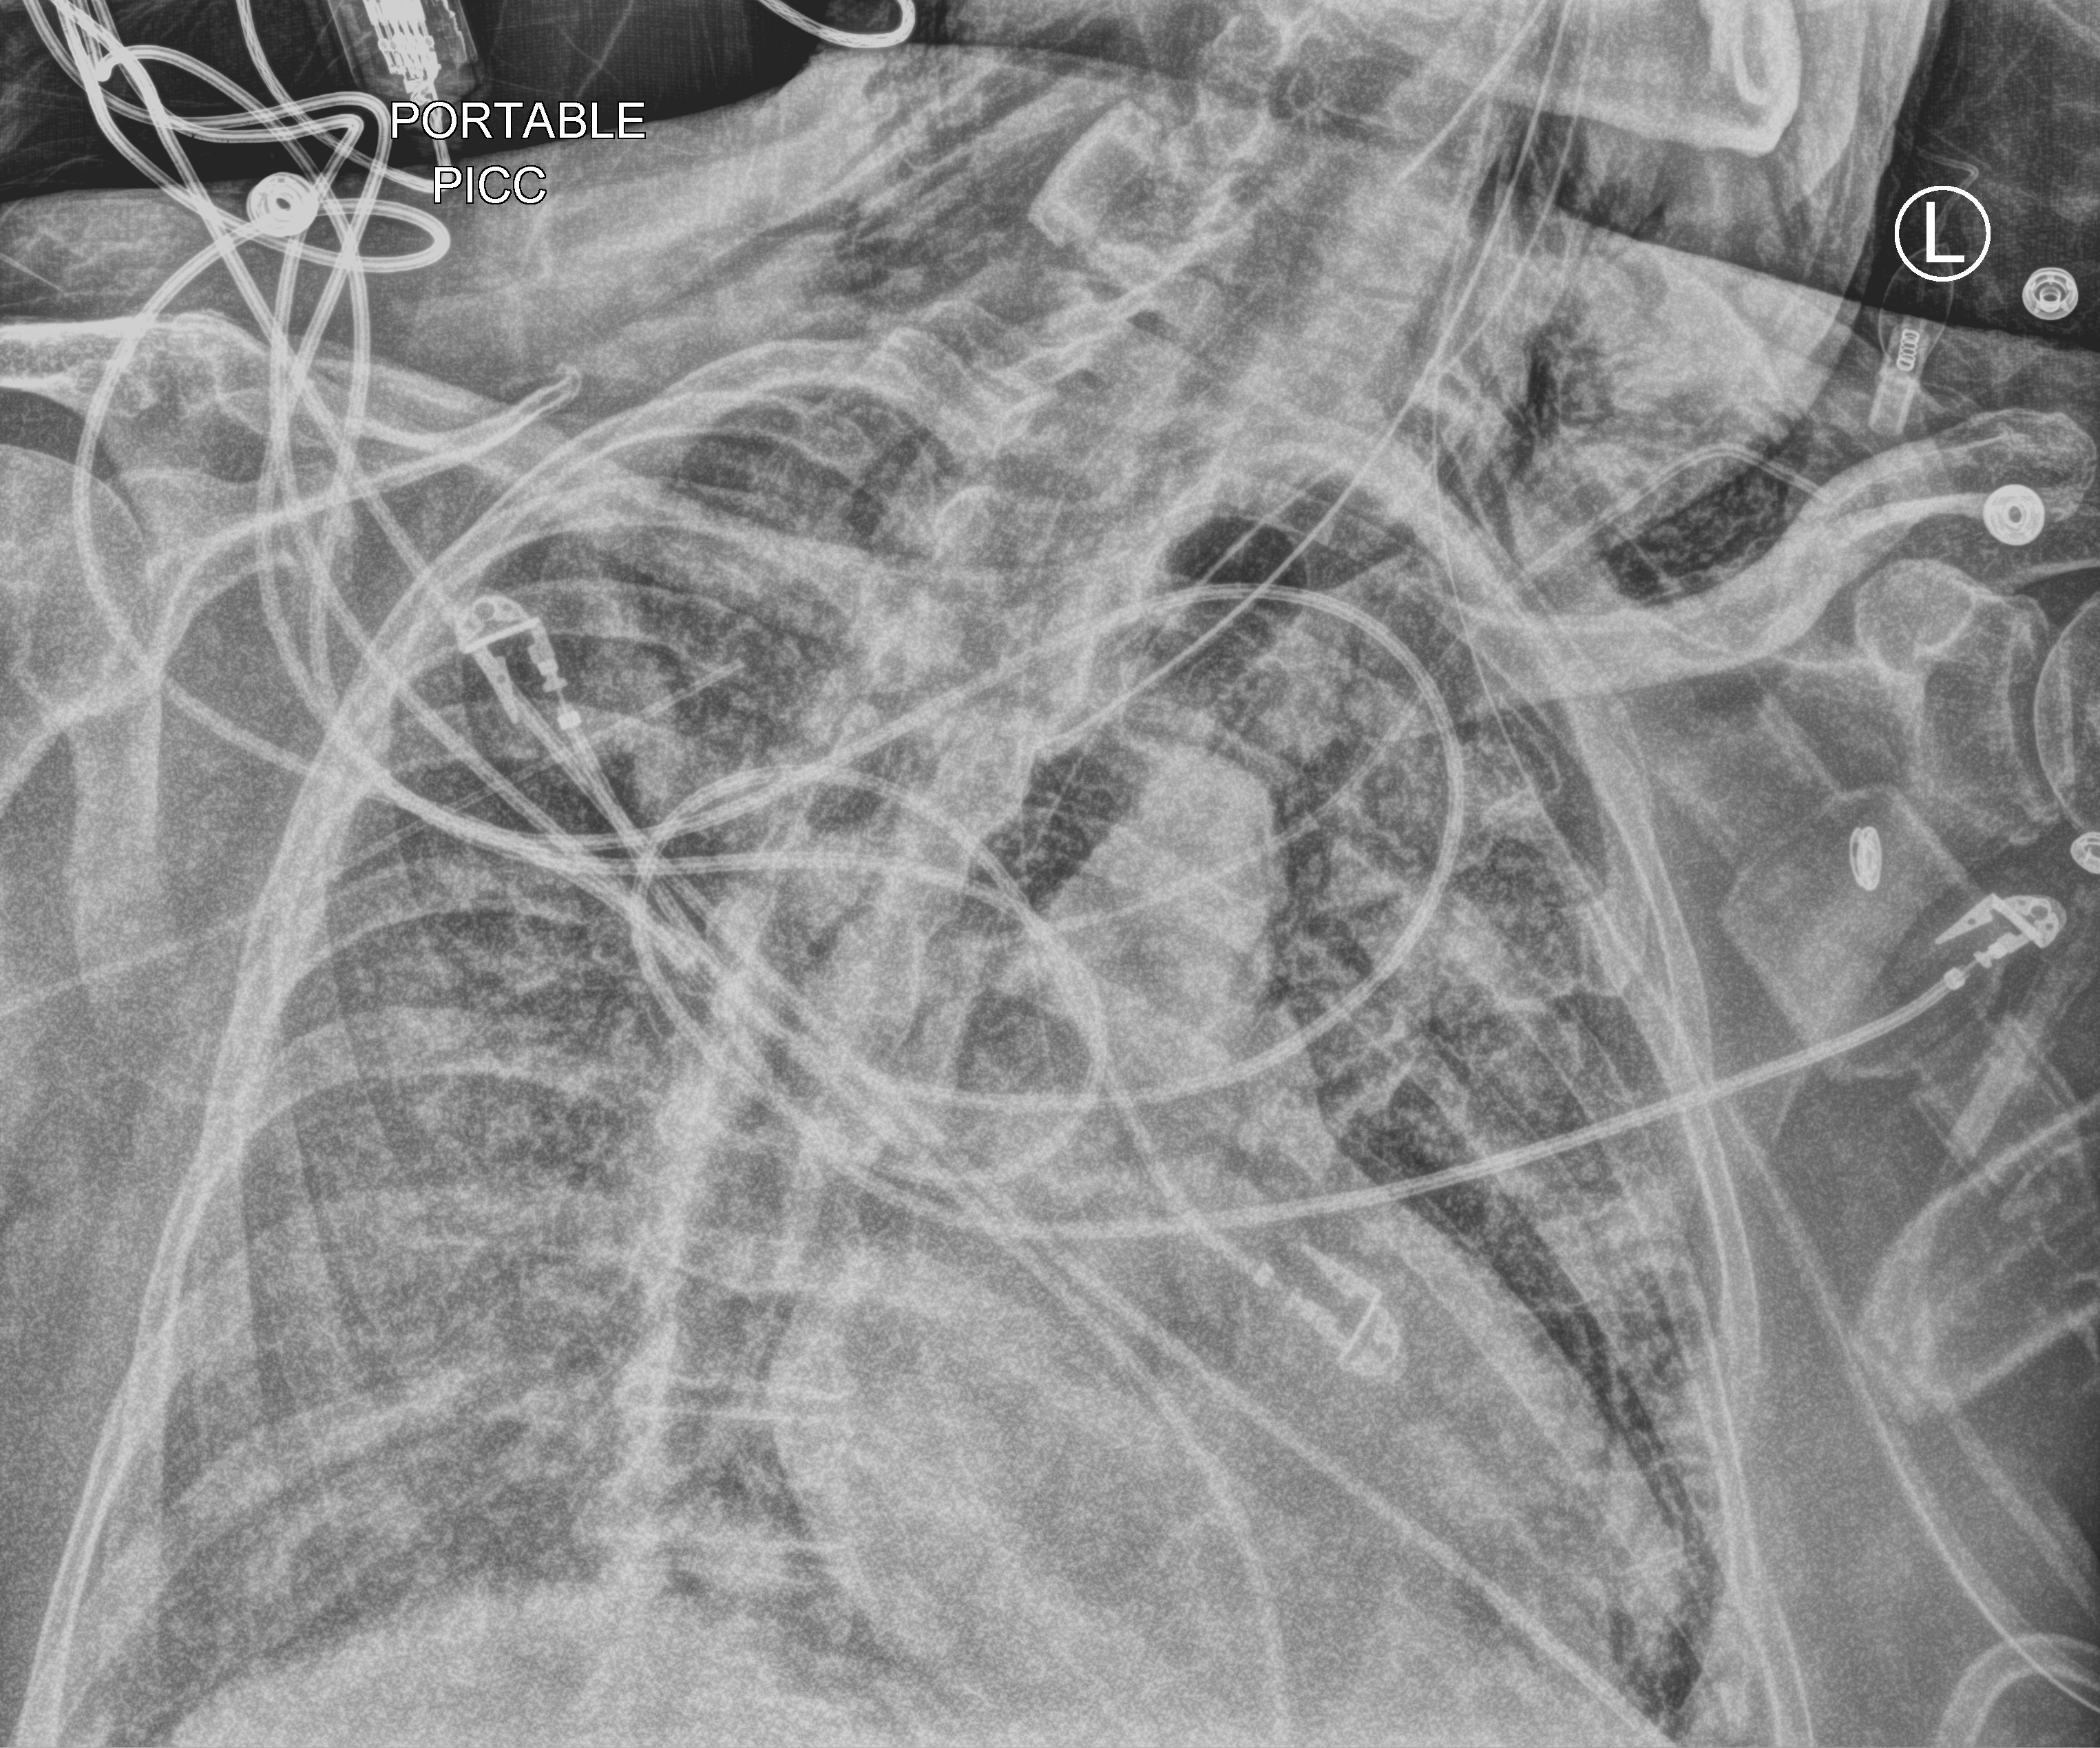
Chest X-ray (portable). Male patient hospitalised with COVID-19, age 75–90 years.
Admission-level facts for this patient (not findings on this image; timing relative to this image not recorded):
- mechanically ventilated during this hospital stay: yes
- hypertension (admission record): yes
- diabetes (admission record): no